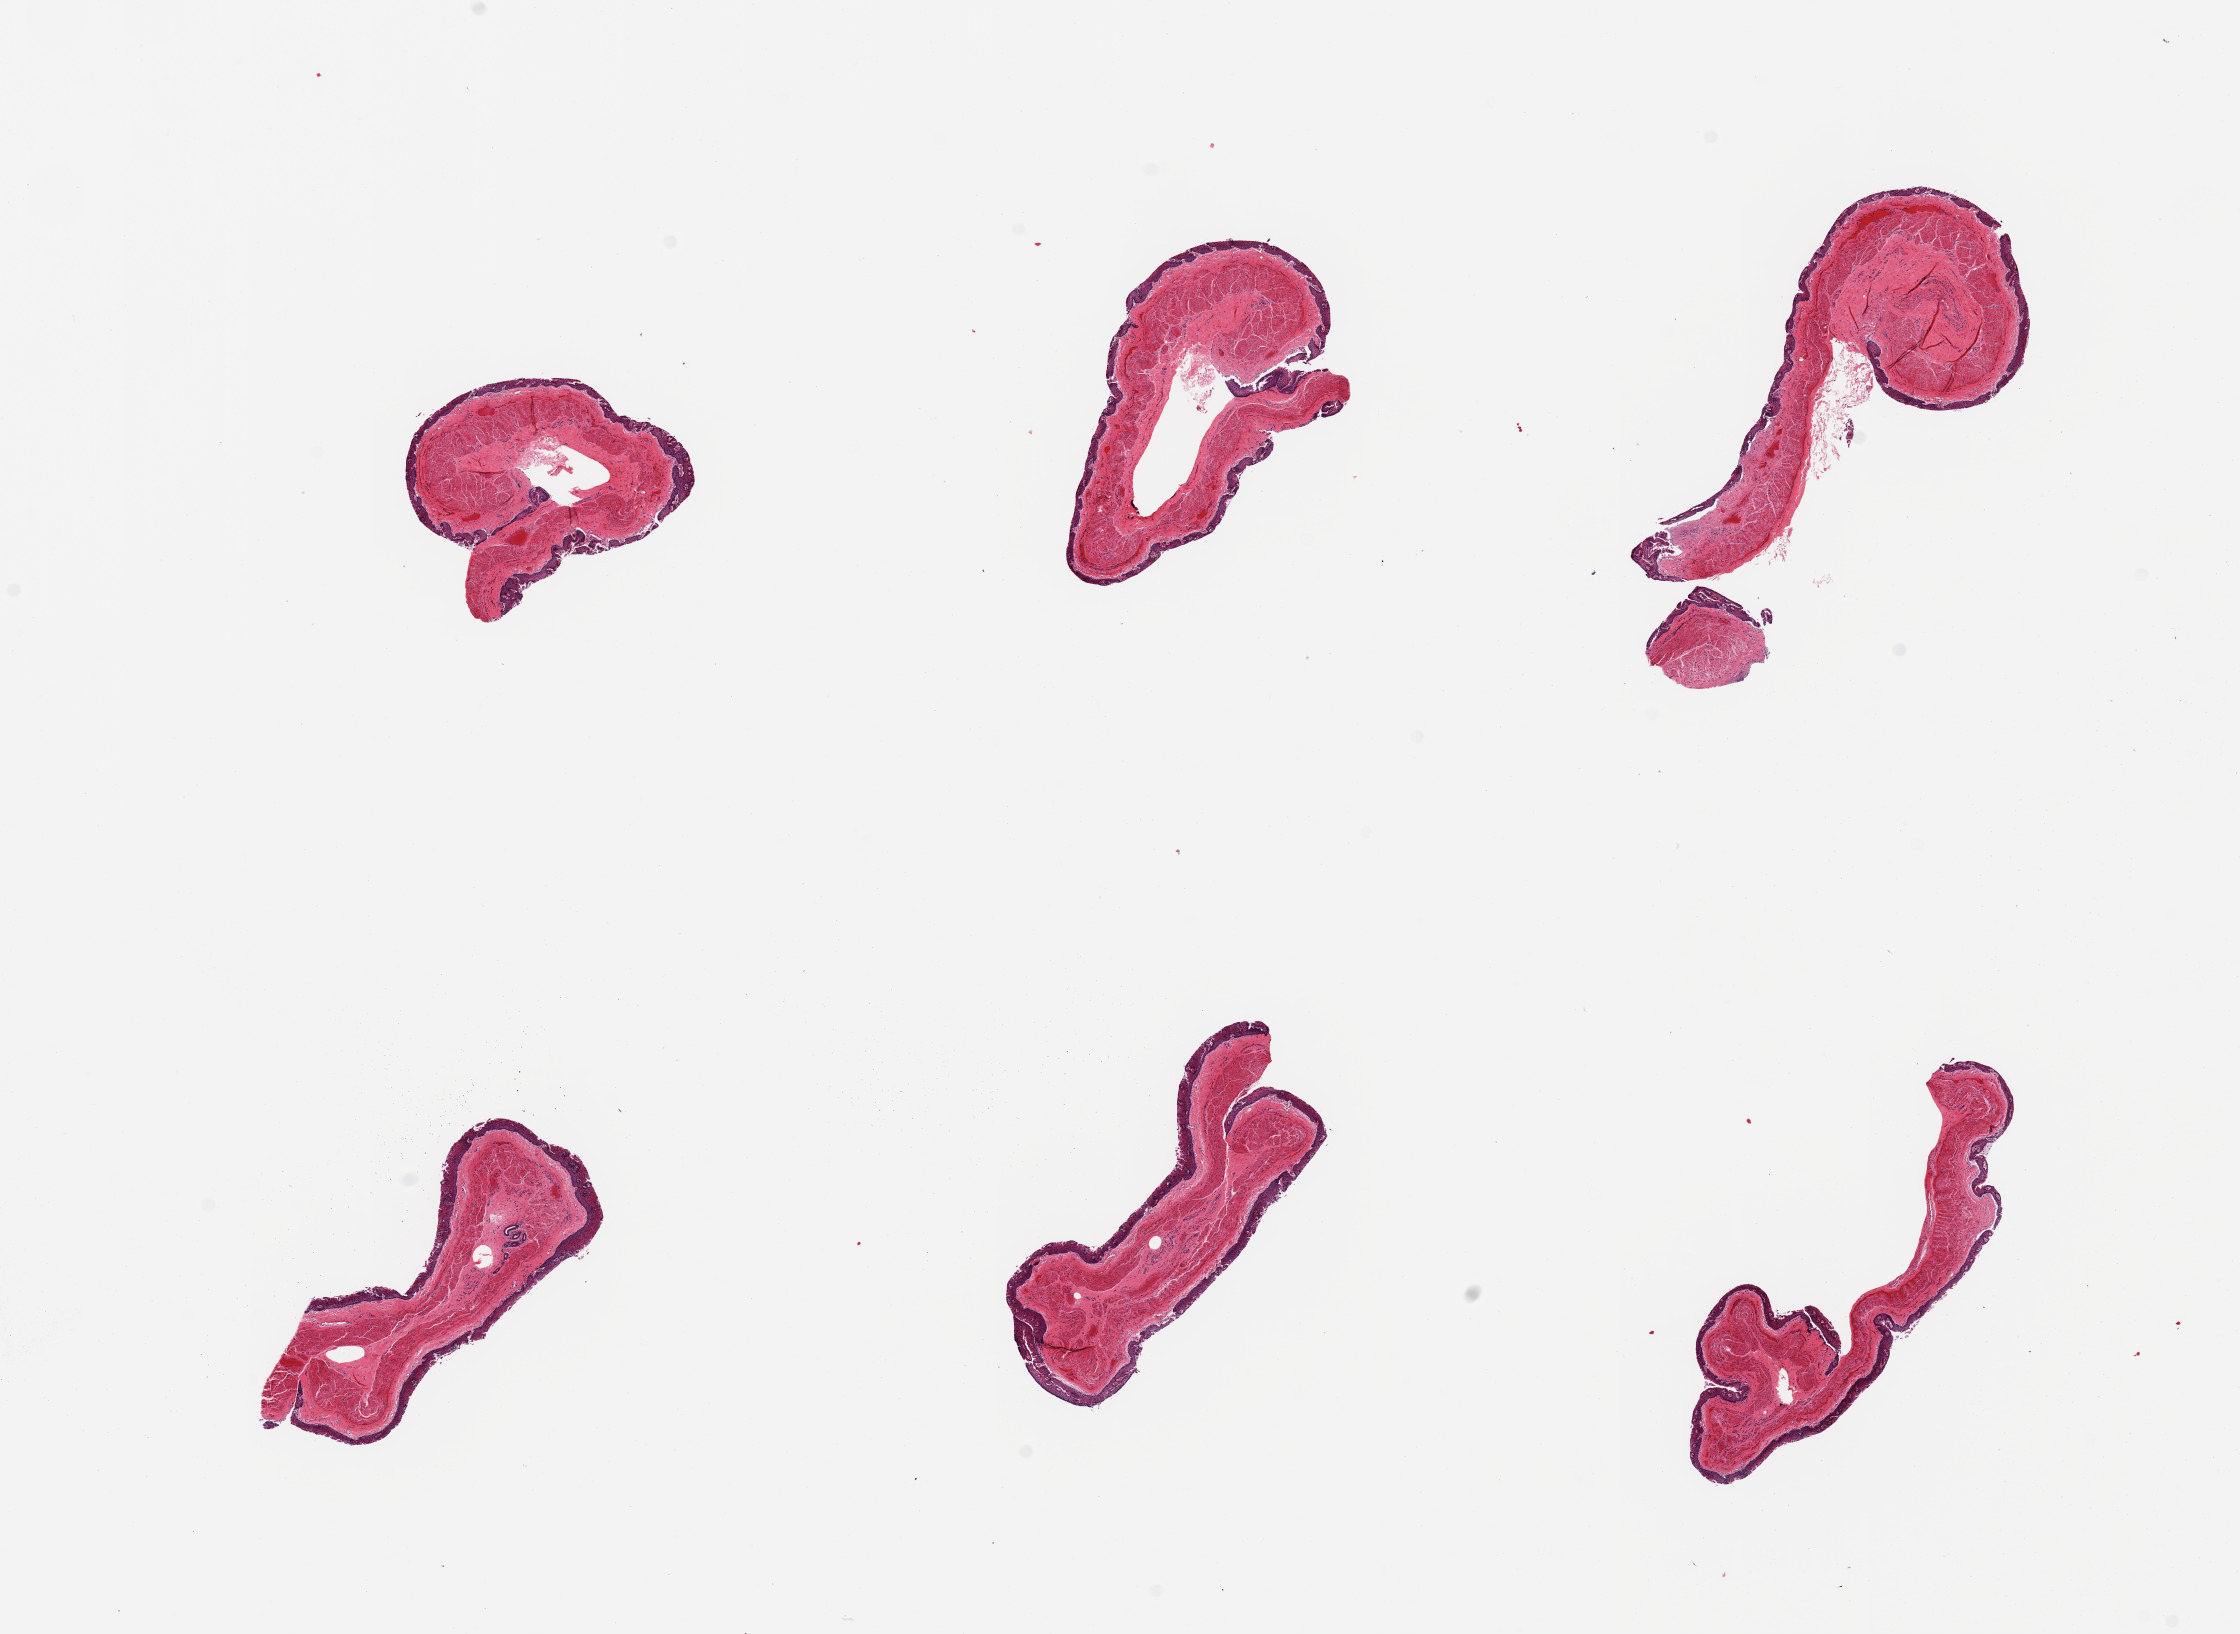
Digitized haematoxylin and eosin-stained section — shown as a low-resolution overview of the whole scanned area (about 17.7 x 12.9 mm, from a 20x scan), PAXgene-fixed paraffin-embedded (PFPE) section, target tissue: esophageal mucous membrane, tissue donor sample. Donor sex: female.
Pathologist's review note for this sample: 6 pieces; squamous epithelium partly fragmented; well trimmed.